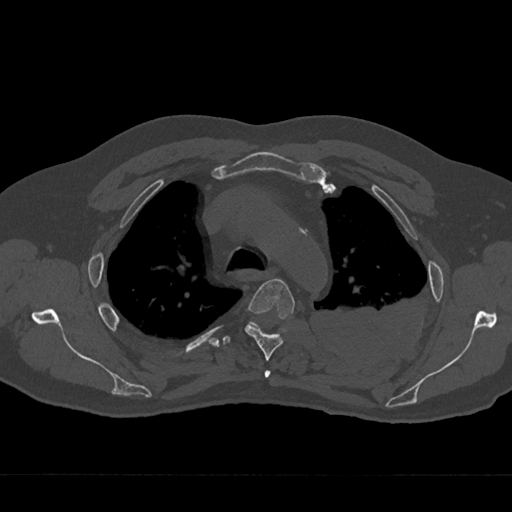
CT including the spine, one axial slice. Position 516 of 797 along the scan axis. Bone window (W 1800 / L 400 HU). 512 × 512 image matrix, field of view 377 × 377 mm. Male patient, age 75 years. Case-level facts recorded for this patient, not image findings: primary cancer: renal; vertebrae with lytic lesions (as recorded): T4.
Annotated regions visible in this slice (semi-automatically segmented with operator editing):
- T3 vertebra: bounding box [x1, y1, x2, y2] px = [264, 370, 271, 378]
- T4 vertebra: [245, 278, 295, 361]
- T5 vertebra: [223, 322, 259, 345]